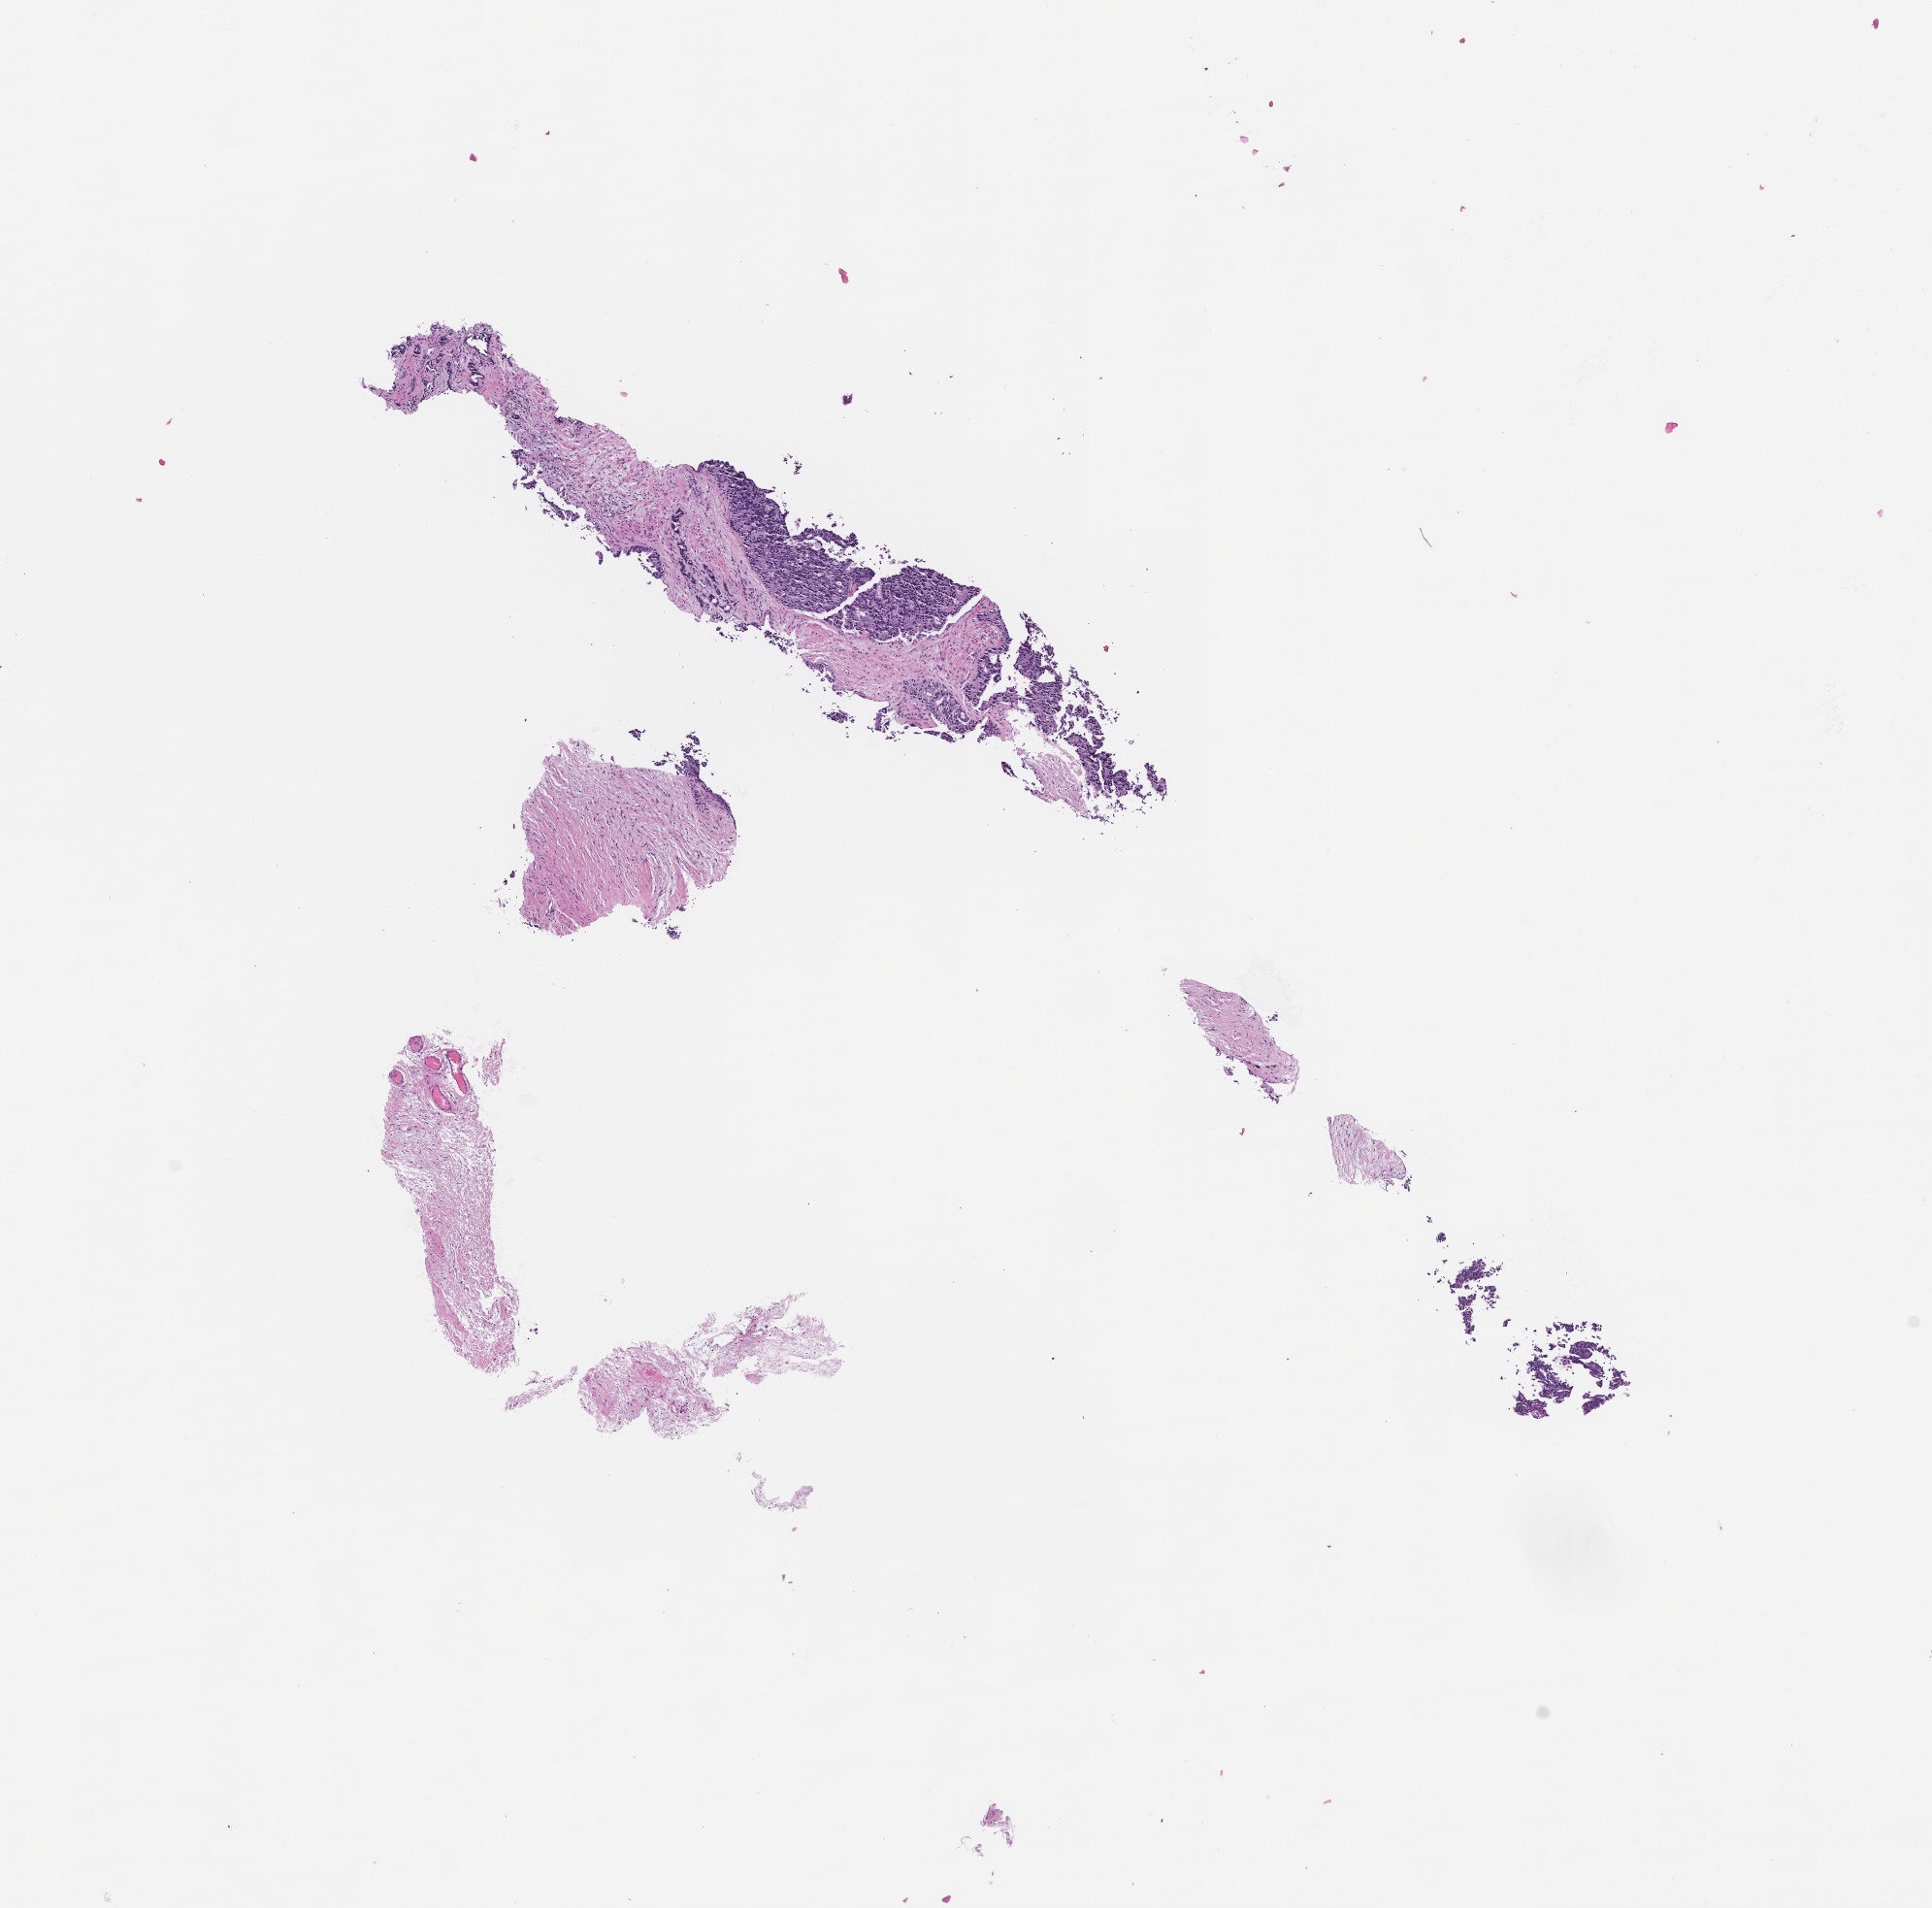
Whole-slide image, H&E stain, shown as a low-resolution overview of the whole scanned area (about 8.0 x 7.9 mm), formalin-fixed, paraffin-embedded (FFPE) tissue, tissue site: prostate, specimen time point: archival tissue. Patient sex: male.
* this section: primary tumor
* diagnosis: Prostate Carcinoma